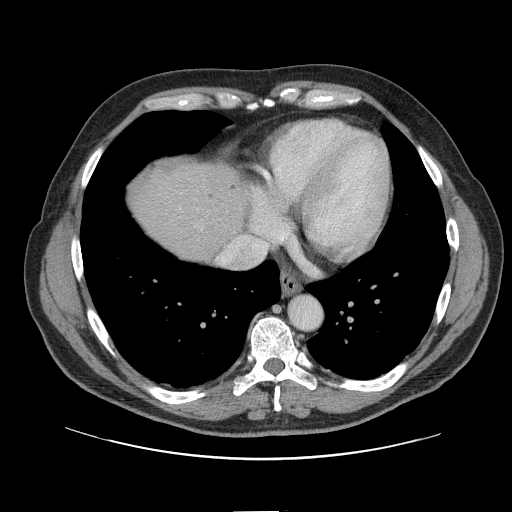
Contrast-enhanced abdominal CT, one axial slice. Position 138 of 161 along the scan axis. 120 kVp. Soft-tissue window (W 400 / L 40 HU). 512 × 512 image matrix, field of view 412 × 412 mm. Male patient, age 66 years. From the clinical record (not read from this slice): diagnosis: colorectal cancer liver metastases, imaged before liver resection; multiple liver metastases: no; largest metastasis: 3.5 cm; disease in both lobes: no.
Annotated regions visible in this slice (expert manual segmentation):
- hepatic veins: bounding box (x1, y1, x2, y2) in pixels: (201, 227, 241, 265)
- liver: (134, 165, 244, 261)
- planned liver remnant (the part of the liver to remain after resection): (133, 165, 244, 261)
- liver metastasis: (231, 184, 238, 192)